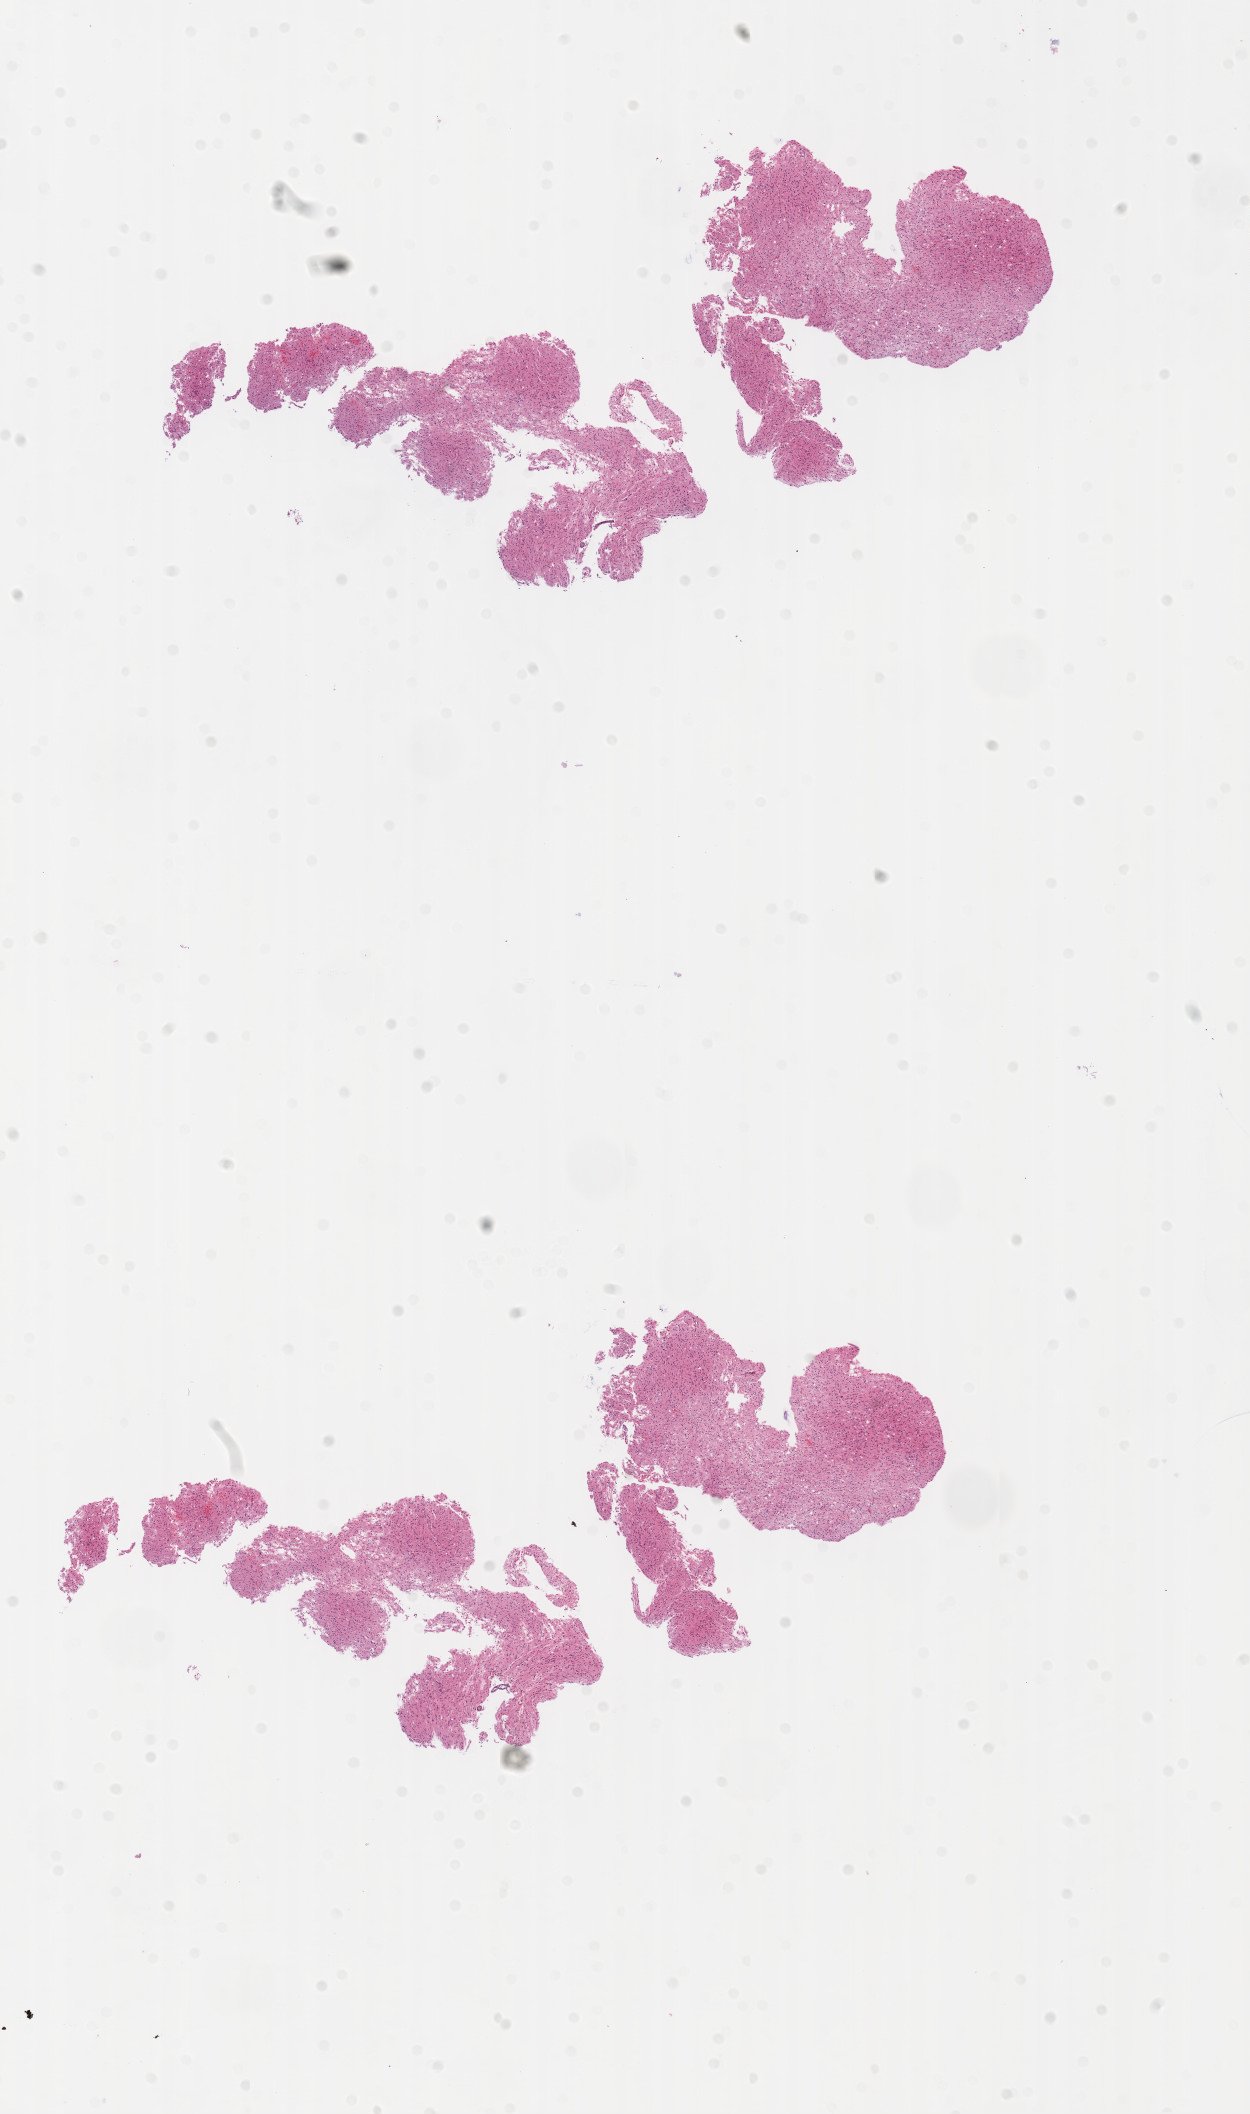
Digitized Hematoxylin and eosin (H&E) stained tissue section (whole slide) — low-resolution overview of the scanned area, about 10.0 x 17.0 mm (from a 20x scan); formalin-fixed paraffin-embedded (FFPE) diagnostic section; primary tumour sample from the brain. Patient: male, age at initial diagnosis 50 years.
• pathologic diagnosis: Glioblastoma